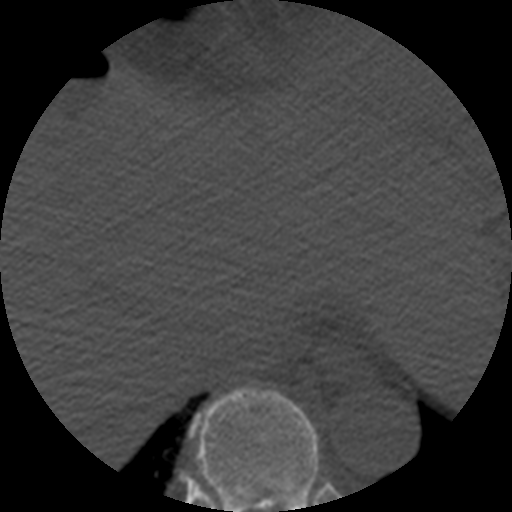
CT including the spine, one axial slice; position 296 of 508 along the scan axis; 120 kVp; bone window (W 1800 / L 400 HU); 1.25 mm slice thickness; 512 × 512 image matrix, field of view 160 × 160 mm. Patient age 57 years. Case-level facts recorded for this patient, not image findings: primary cancer: prostate.
Structures marked on this image (semi-automatic segmentation, software-assisted and operator-edited):
- T9 vertebra: bounding box <190,388,319,512> (left, top, right, bottom; pixels)